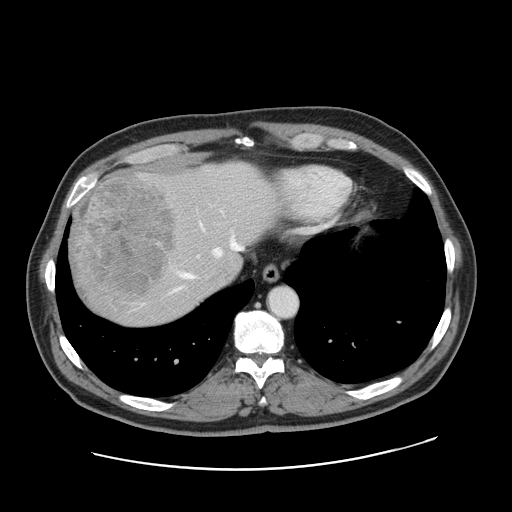
Contrast-enhanced abdominal CT, one axial slice. Position 137 of 178 along the scan axis. 120 kVp. Intravenous contrast given. Soft-tissue window (W 400 / L 40 HU). 512 × 512 image matrix, field of view 403 × 403 mm. Male patient, age 63 years. From the clinical record (not read from this slice): diagnosis: colorectal cancer liver metastases, imaged before liver resection.
Structures marked on this image (expert manual segmentation):
- hepatic veins: bounding box <171,223,243,293> (left, top, right, bottom; pixels)
- liver: <68,160,278,326>
- planned liver remnant (the part of the liver to remain after resection): <171,165,278,281>
- portal vein (with intrahepatic branches): <158,242,161,245>
- liver metastasis: <71,171,176,297>